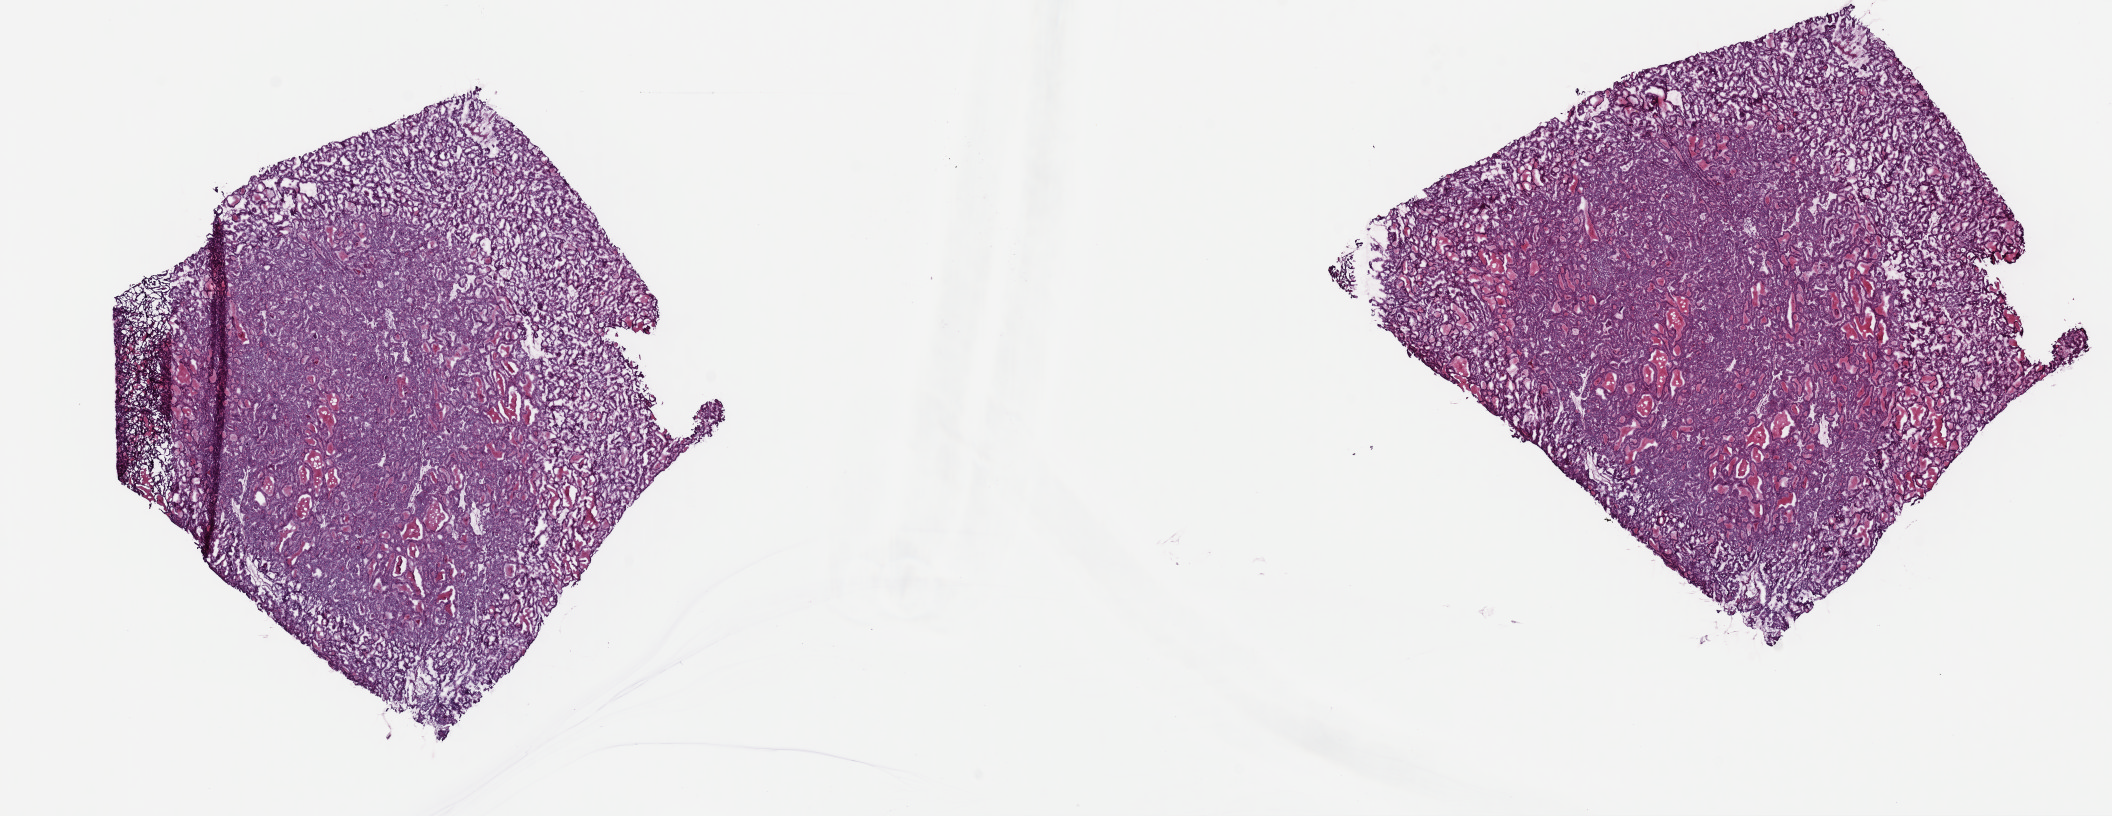
Whole-slide histology image, Hematoxylin and eosin (H&E) stained, shown as a low-resolution overview of the whole scanned area (about 16.7 x 6.4 mm, acquisition: 40x scan); frozen section; thyroid, primary tumour sample. Male, age 70 years at initial diagnosis. Pathologist review of this section (percent, as recorded): tumour cells 100%, tumour nuclei 97%, normal cells 0%, stromal cells 0%, necrosis 0%. Inflammatory infiltration, as recorded: lymphocyte infiltration 0%, monocyte infiltration 0%, neutrophil infiltration 0%.
- lymph nodes positive (case pathology): 16 of 31 examined
- histologic diagnosis: Papillary adenocarcinoma, NOS (thyroid gland)
- AJCC pathologic stage: IVA (7th edition)